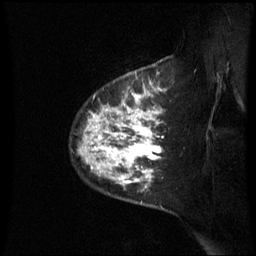
Breast MRI (dynamic contrast-enhanced), one sagittal slice. Dynamic contrast-enhanced series, image 2 of 3 at this slice position (ordered by acquisition). 1.5 T. TE 4.2 ms, TR 8.9 ms. 2.4 mm slice thickness. 256 × 256 image matrix, field of view 210 × 210 mm. Patient: female, 42 years. Case-level facts recorded for this patient, not image findings: setting: breast cancer imaged before/during neoadjuvant chemotherapy; receptor status: HER2-positive.
Annotated regions visible in this slice (semi-automatically segmented with operator editing):
- analysis volume of interest (the breast-tissue region the enhancement analysis was run in; not a lesion): bounding box [x1, y1, x2, y2] px = [79, 93, 166, 210]
- tumour enhancement mask (voxels above the 70 % enhancement threshold inside the analysis volume of interest): [79, 93, 163, 189]